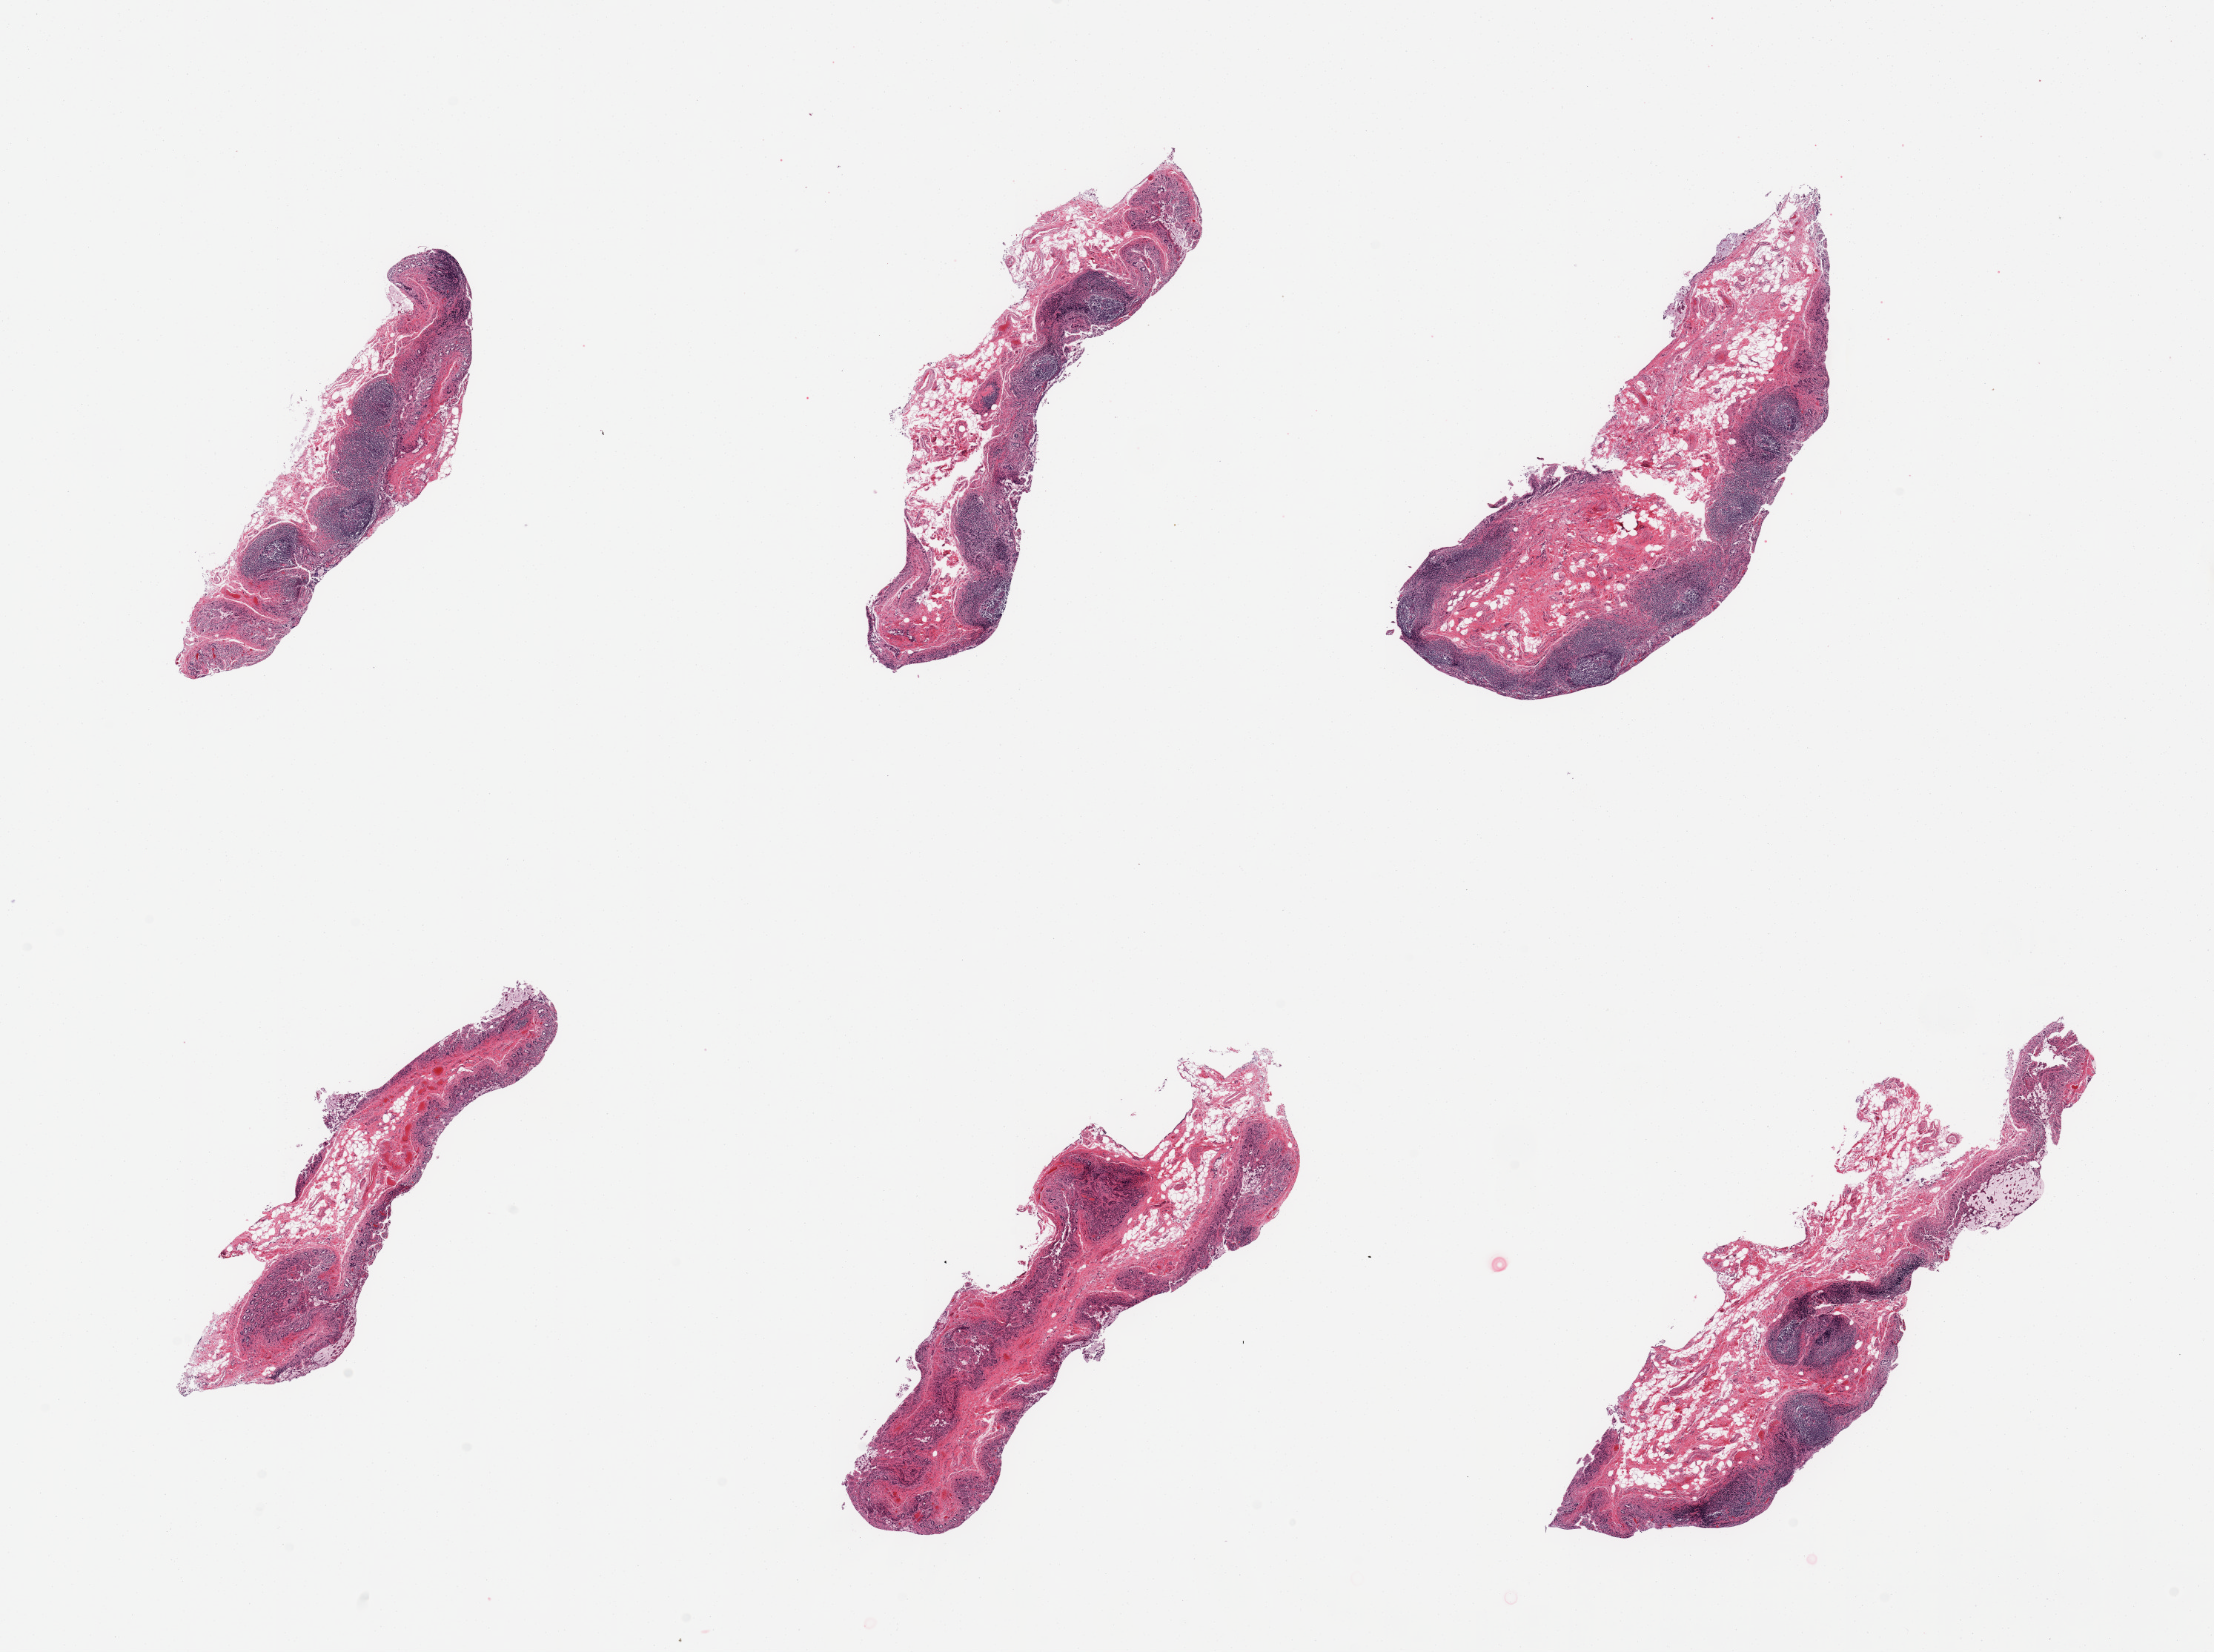
H&E whole-slide image, brightfield — shown as a low-resolution overview of the whole scanned area (about 23.6 x 17.6 mm). PAXgene-fixed paraffin-embedded (PFPE) section. Sampled site (target tissue): ileum. Donor tissue sample.
Reviewer comment on this tissue sample: 6 pieces, glandular mucosa sloughed but target lymphoid aggregates are ~30% of residual tissue.